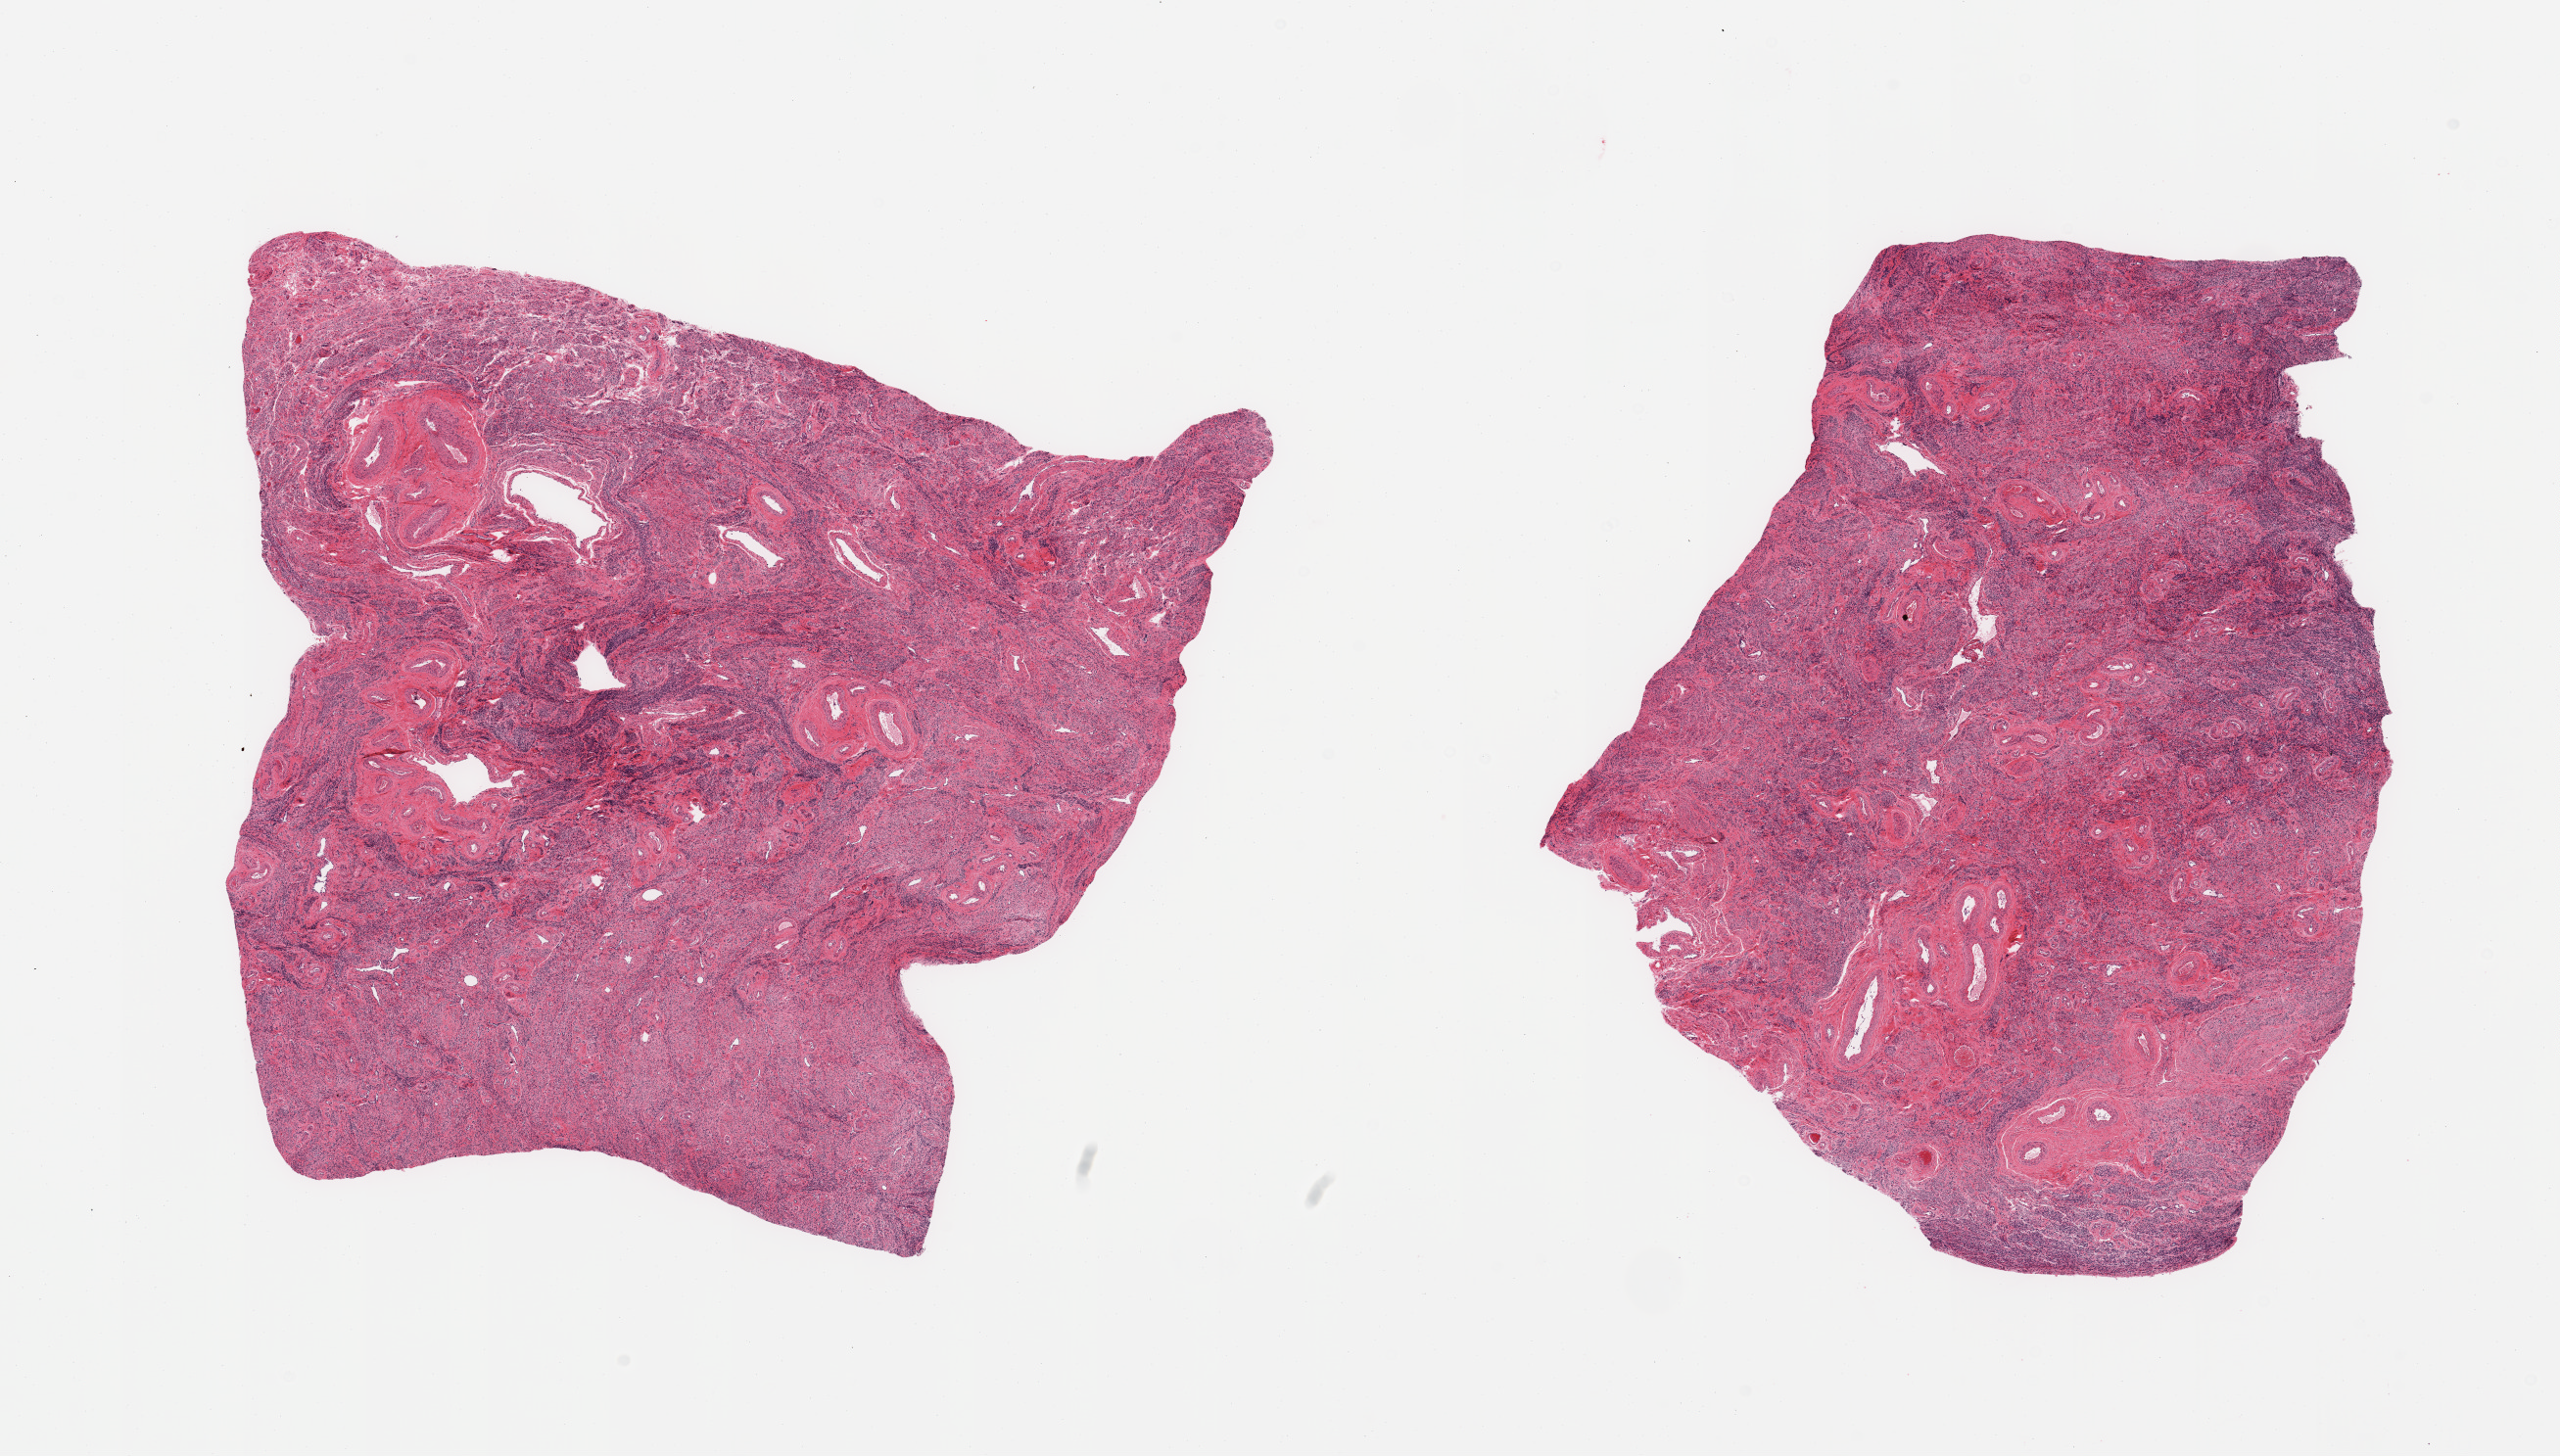
Digitized hematoxylin and eosin (H&E)-stained section, brightfield — a low-resolution overview of the entire scanned area, about 20.7 x 11.8 mm; PAXgene-fixed paraffin-embedded (PFPE) section; target tissue: uterus; tissue donor sample. Female donor.
Review note (as recorded): 2 pieces; no glands all myometrium in this cut.